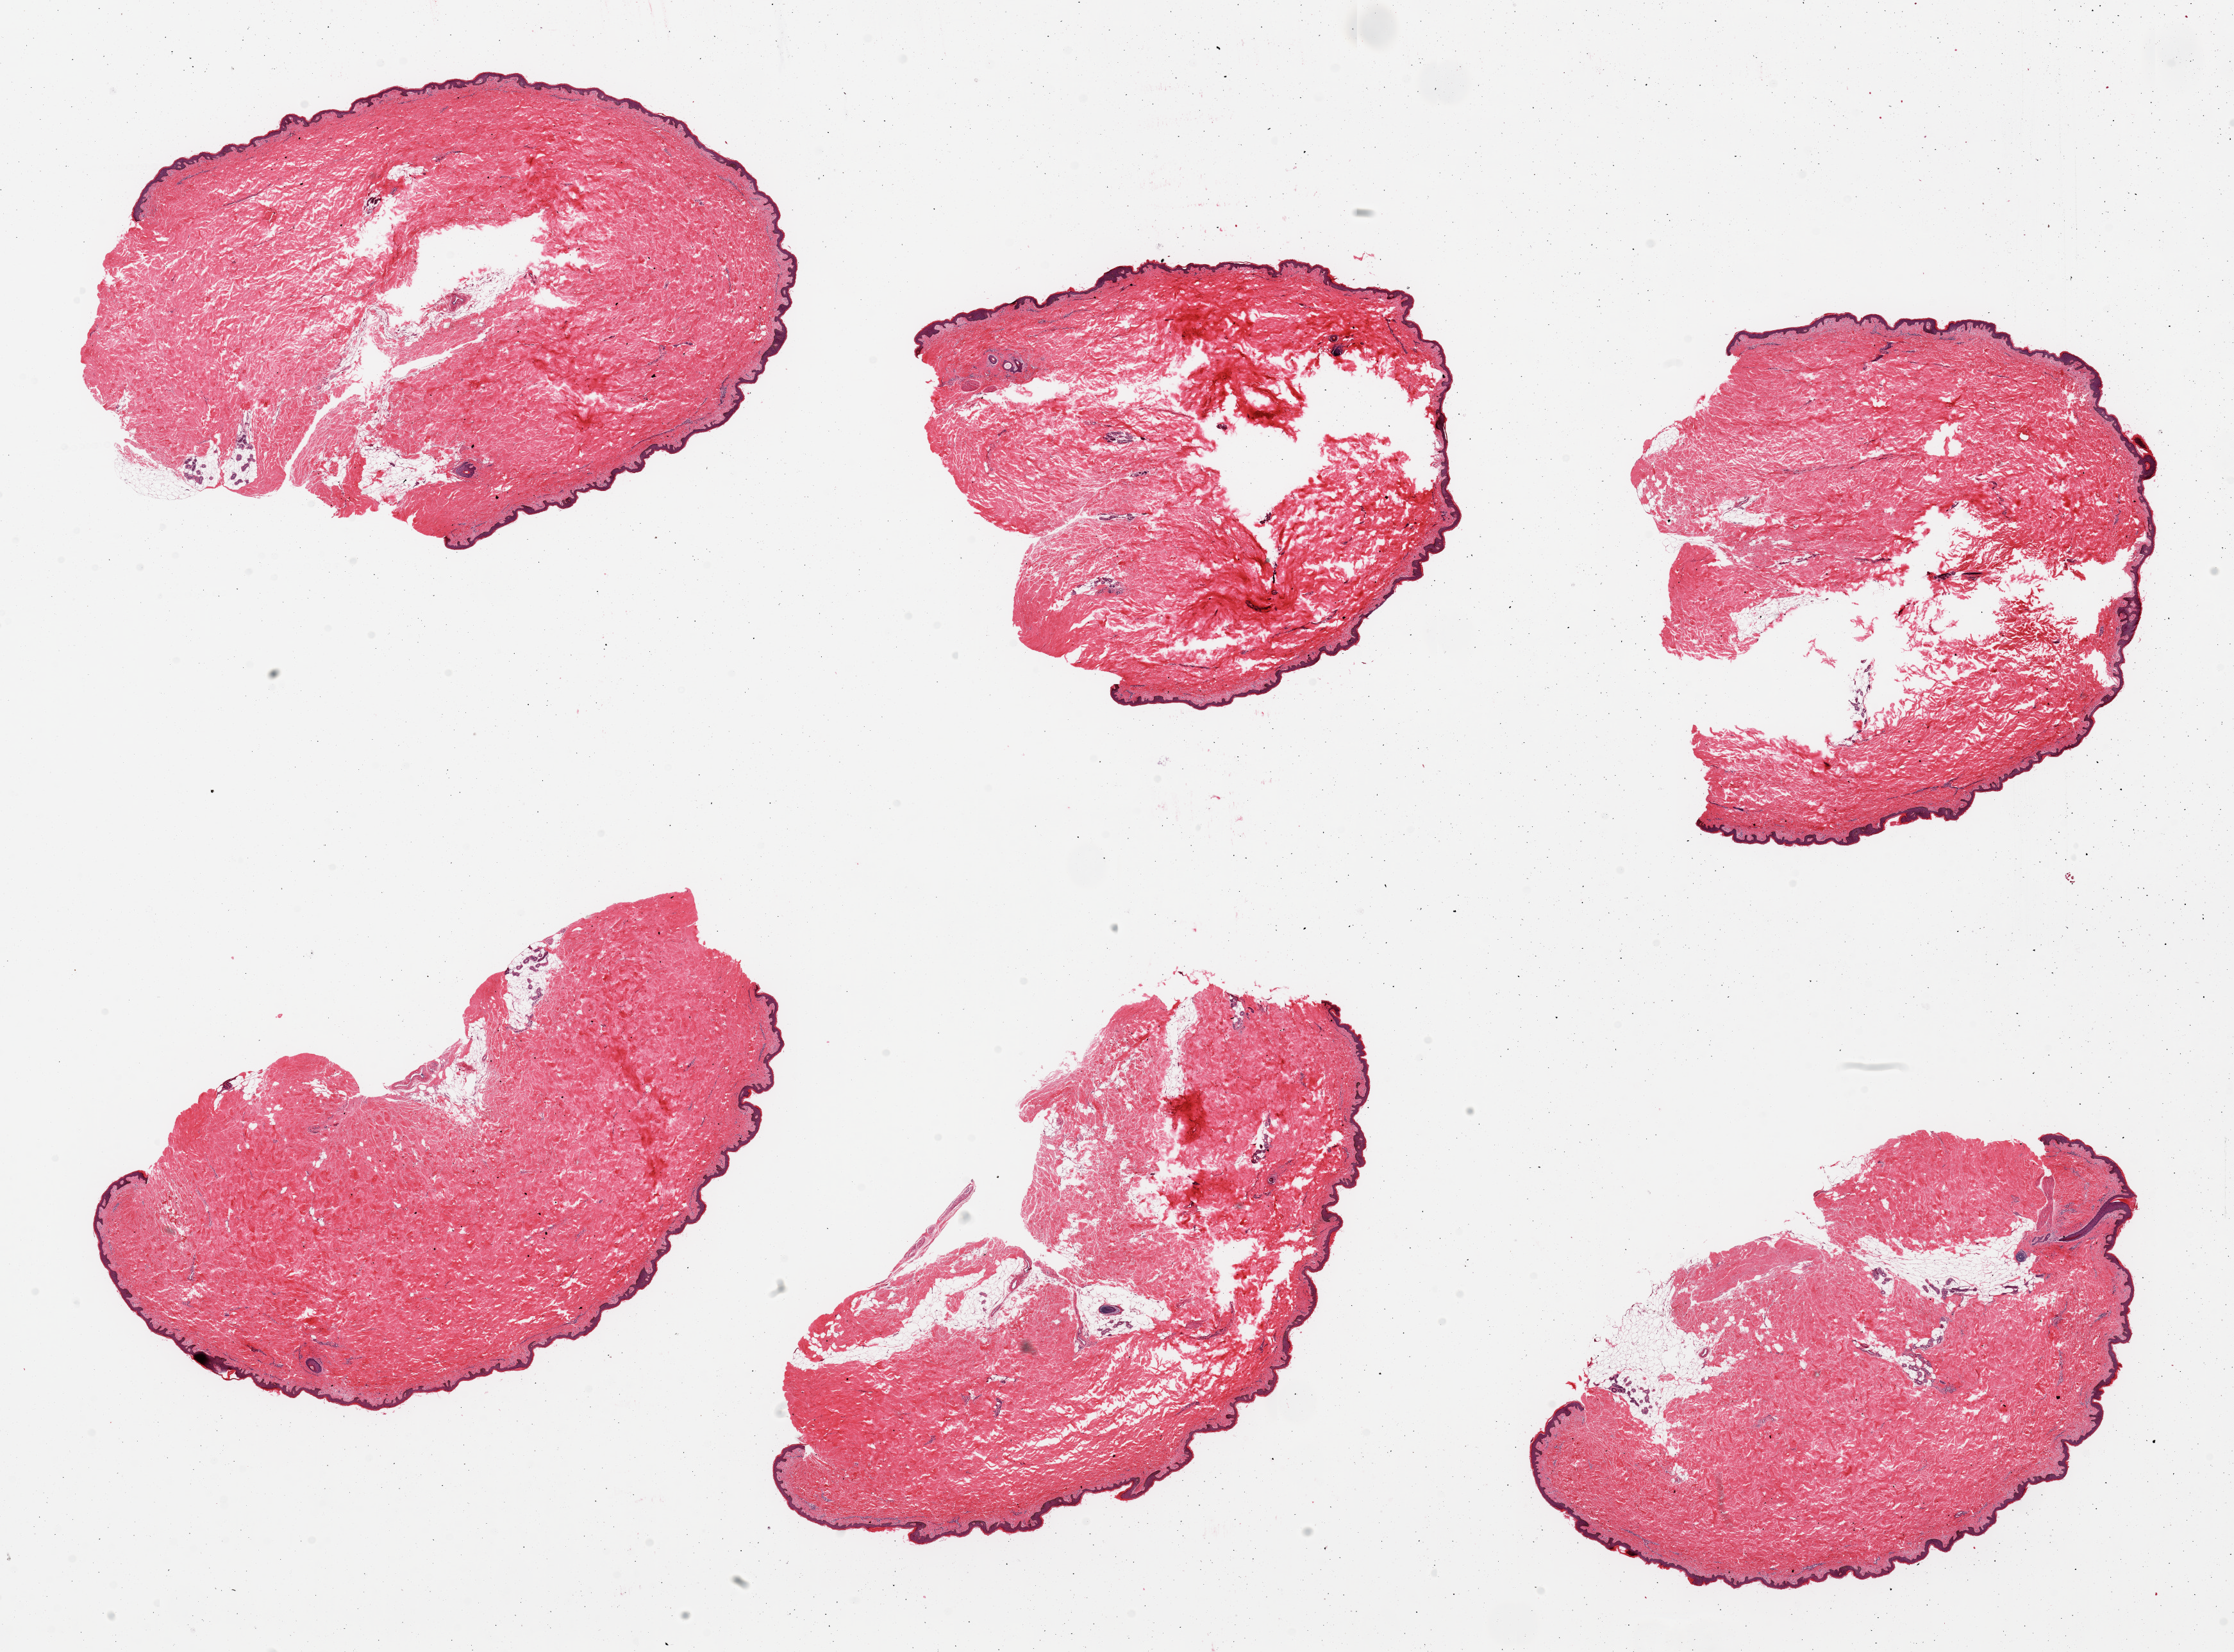
Digitized haematoxylin and eosin-stained section, low-resolution overview of the scanned area, about 27.6 x 20.4 mm (slide scanned at 20x), PAXgene-fixed paraffin-embedded (PFPE) section, sampled site (target tissue): skin of suprapubic region, tissue donor sample. Female donor.
Review note (as recorded): 6 pieces, minimal dermal fat; squamous epithelium is ~40 microns.